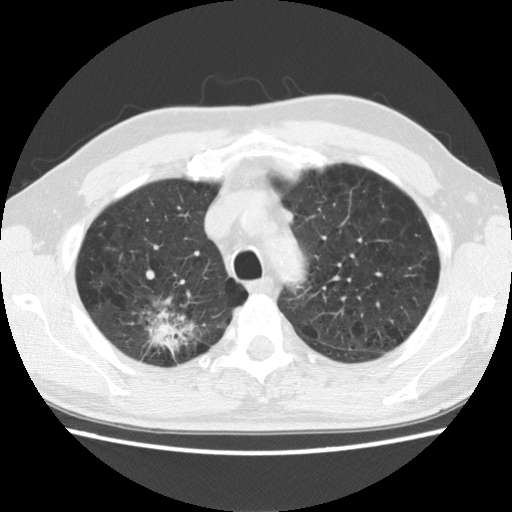
Axial slice from a low-dose chest CT screening exam. Baseline annual screen. Lung window (W 1500 / L -600 HU). 512 × 512 image matrix. Male, age 64 years at enrolment. Former smoker at enrolment.
• Expert reader's lesion annotation, bounding box <115,295,205,366> (left, top, right, bottom; pixels).
• Screening reader's record for this exam (one nodule recorded; not confirmed to be the boxed lesion): non-calcified nodule or mass ≥4 mm, right upper lobe, 39 × 31 mm, spiculated (stellate) margins, mixed attenuation.
• Official screen result: positive, change unspecified: nodule(s) >= 4 mm or enlarging nodule(s), mass(es), or other non-specific abnormalities suspicious for lung cancer.
• Participant outcome: lung cancer diagnosed 74 days after this screen — adenocarcinoma, NOS, right upper lobe, moderately differentiated (G2), stage IB (AJCC 6th edition), 40 mm at pathology.